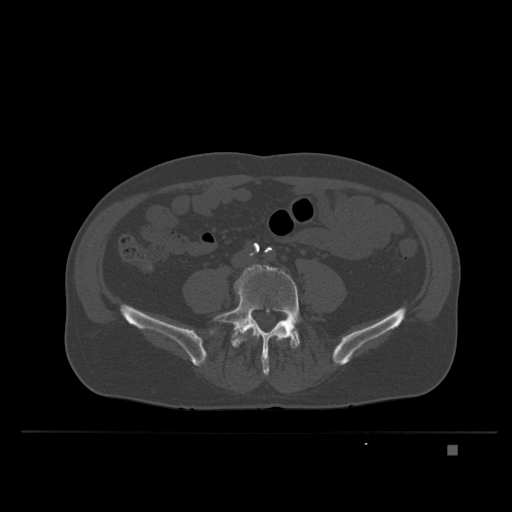
CT including the spine, one axial slice; position 59 of 435 along the scan axis; bone window (W 1800 / L 400 HU); 1.5 mm slice thickness; 512 × 512 image matrix. Male patient, age 73 years. Case-level facts recorded for this patient, not image findings: primary cancer: skin.
Structures marked on this image (semi-automatically segmented with operator editing):
- L4 vertebra: bounding box <247,328,254,332> (left, top, right, bottom; pixels)
- L5 vertebra: <213,264,302,375>